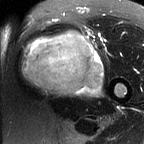
MRI of an extremity soft-tissue mass, one axial slice; slice 40 of 60 in the series (ordered by position); T2-weighted fat-saturated; MR volume resampled by the dataset authors to the PET/CT grid (not the native acquisition matrix); 3.27 mm slice thickness; 144 × 144 image matrix, field of view 141 × 141 mm. Female patient. Case-level facts recorded for this patient, not image findings: histological type: pleiomorphic leiomyosarcoma; grade: intermediate; site of the primary tumour: left thigh.
Structures marked on this image (expert contour drawn on MRI and transferred to this co-registered scan by the dataset authors):
- gross tumour volume including surrounding oedema: box from (x=20, y=31) to (x=103, y=98) px
- gross tumour volume (mass): (x=20, y=31)–(x=103, y=98)